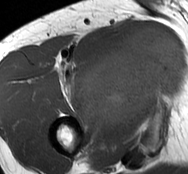
MRI of an extremity soft-tissue mass, one axial slice; slice 58 of 93 in the series (ordered by position); MR volume resampled by the dataset authors to the PET/CT grid (not the native acquisition matrix); 3.27 mm slice thickness; 188 × 174 image matrix, field of view 184 × 170 mm. Male patient. Case-level facts recorded for this patient, not image findings: histological type: undifferentiated - pleiomorphic; grade: high; site of the primary tumour: right thigh.
Structures marked on this image (expert contour drawn on MRI and transferred to this co-registered scan by the dataset authors):
- gross tumour volume including surrounding oedema: bounding box <77,26,185,130> (left, top, right, bottom; pixels)
- gross tumour volume (mass): <77,26,185,130>